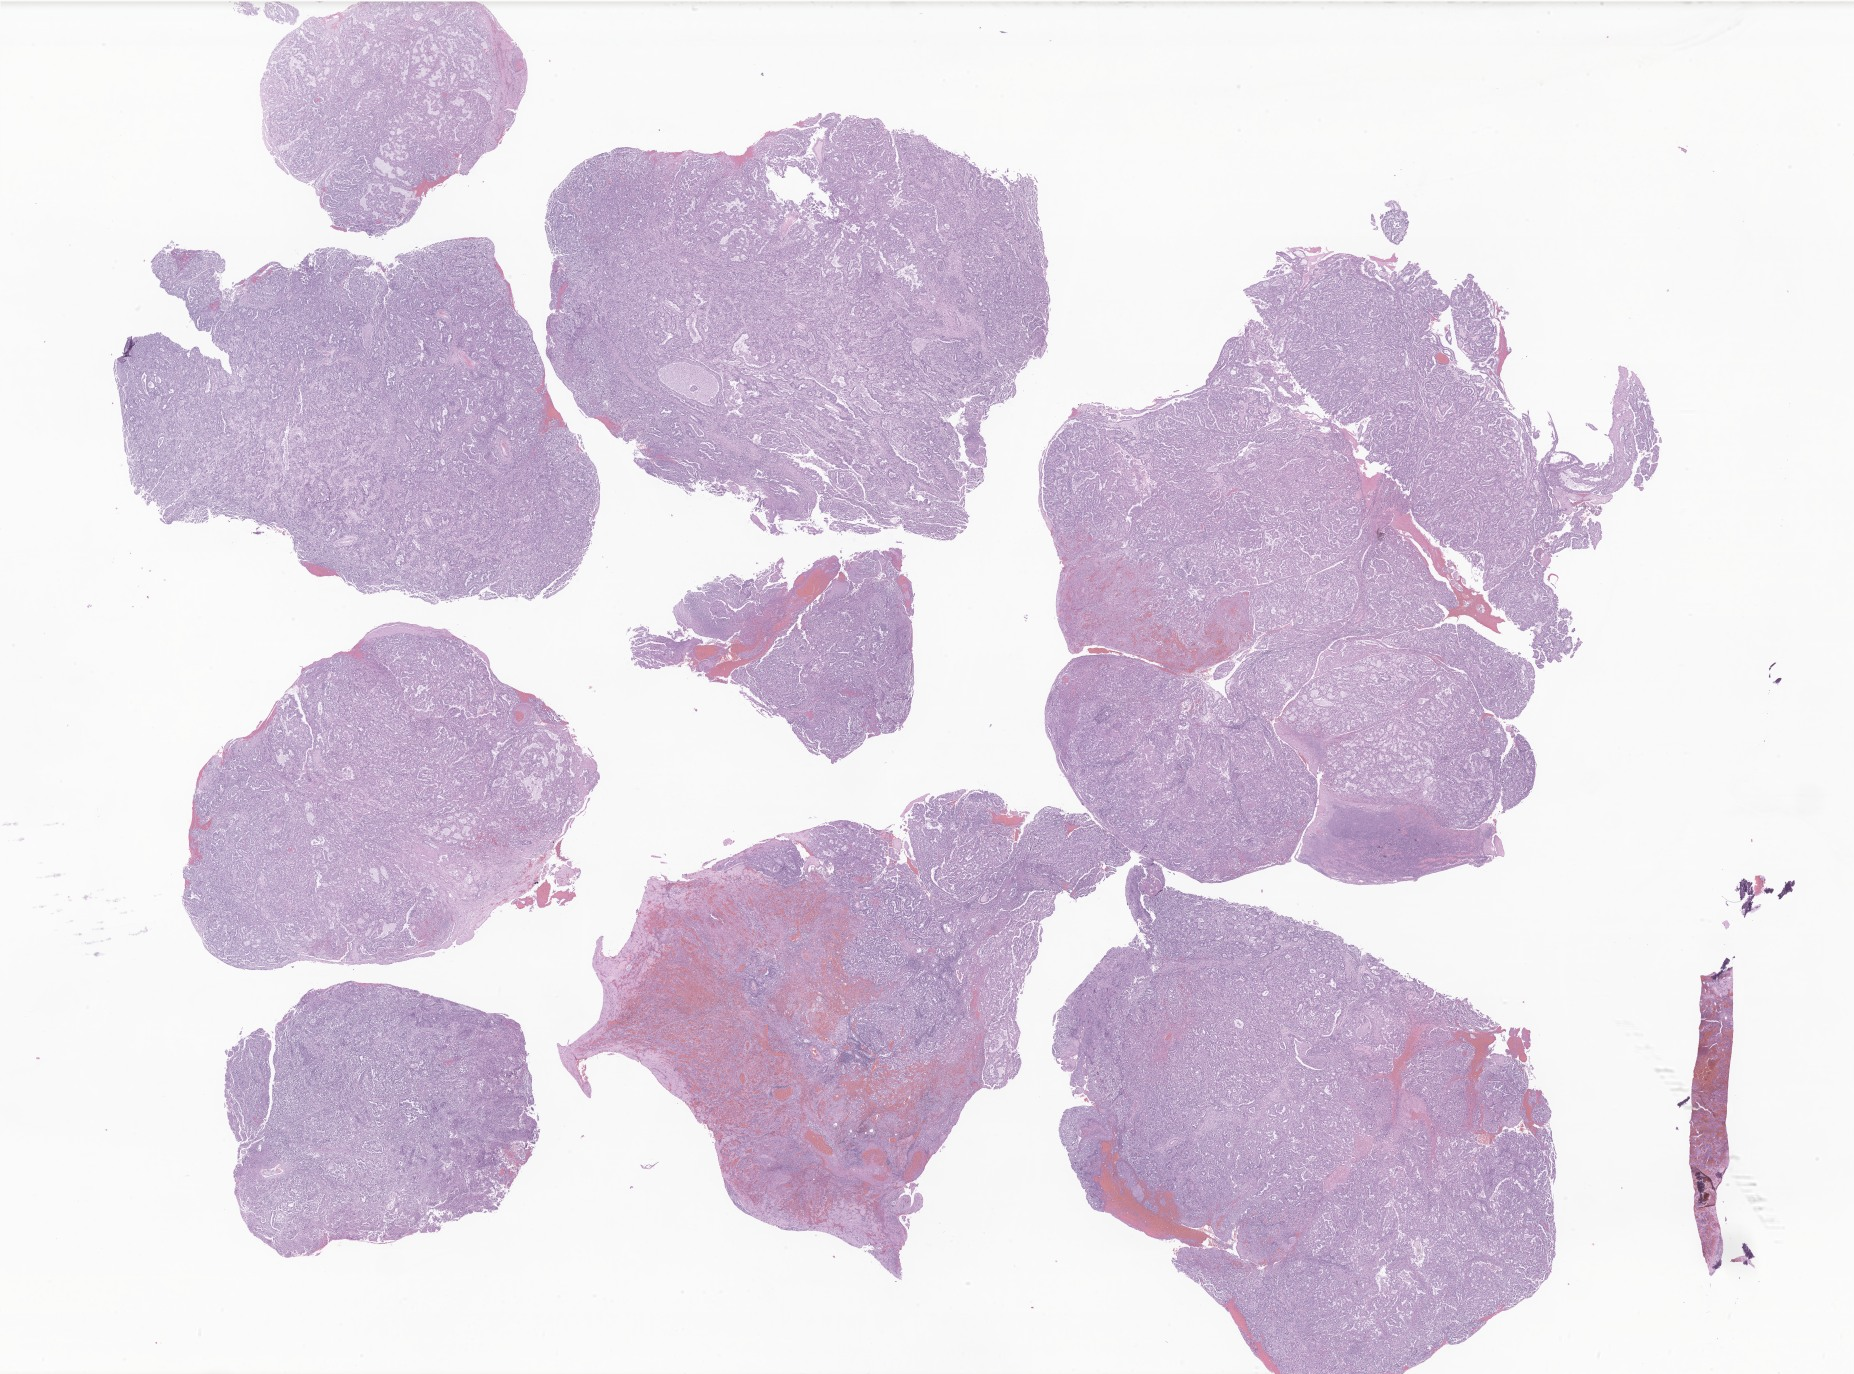
Whole-slide image, hematoxylin and eosin (H&E) stain of tumor tissue from the vagina, whole scanned area (about 31.3 x 23.2 mm) shown as a low-resolution overview; FFPE section. Female patient, age 168 months (14 years).
Diagnosis: Adenocarcinoma, NOS.